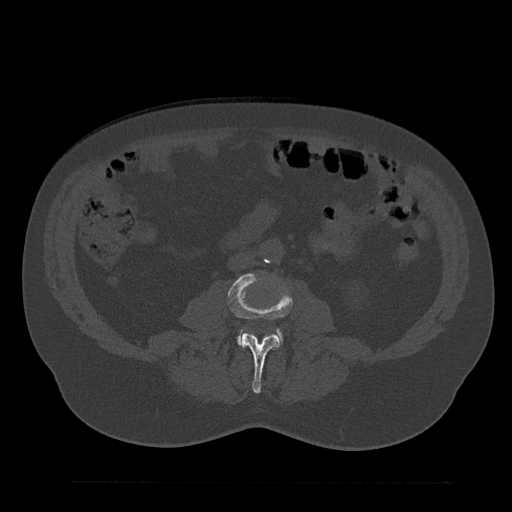
CT including the spine, one axial slice; position 12 of 797 along the scan axis; bone window (W 1800 / L 400 HU); 512 × 512 image matrix, field of view 430 × 430 mm. Male patient, age 61 years. Case-level facts recorded for this patient, not image findings: primary cancer: prostate.
Structures marked on this image (semi-automatically segmented with operator editing):
- L3 vertebra: bounding box (x1, y1, x2, y2) in pixels: (228, 272, 292, 394)
- L4 vertebra: (237, 332, 282, 345)